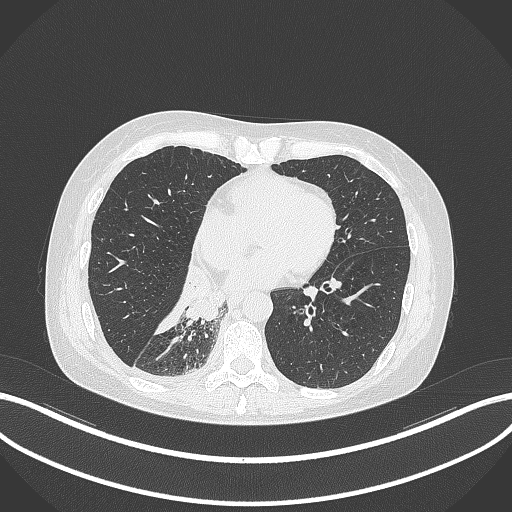
Chest CT, one axial slice; position 116 of 329 along the scan axis; lung window (W 1500 / L -600 HU); 512 × 512 image matrix. Female patient, age 63 years. From the clinical record (not read from this slice): clinical TNM (as recorded): T1c N0 M0.
Outlined on this slice (bounding box drawn by a radiologist):
- lung tumour (recorded histology: adenocarcinoma): bounding box <180,268,224,323> (left, top, right, bottom; pixels)